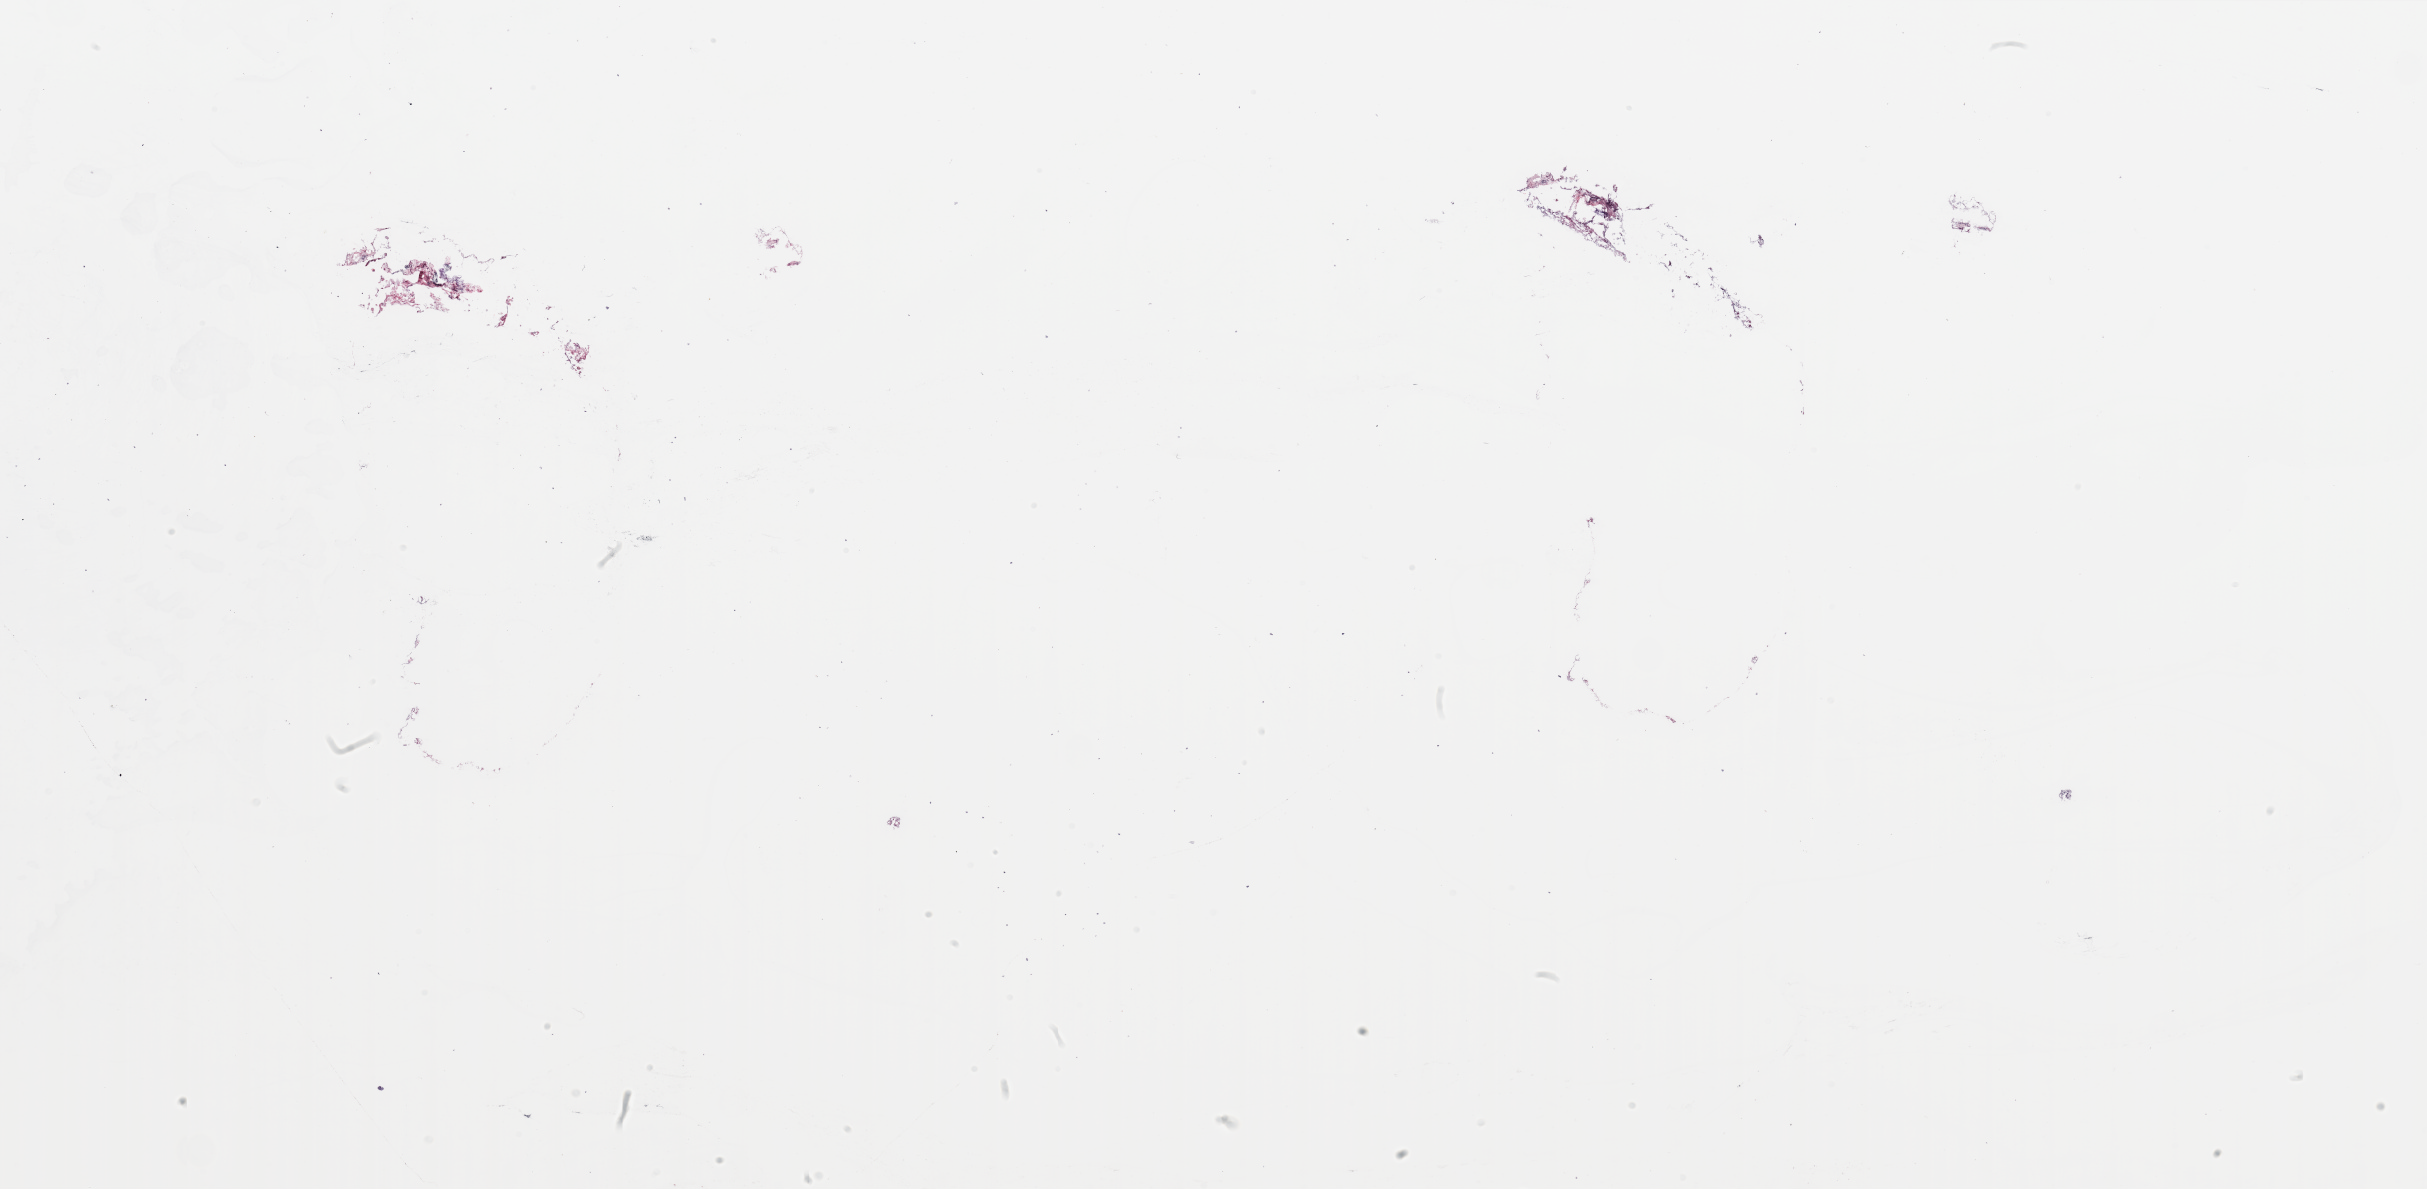
Whole-slide histology image, H&E-stained, whole scanned area (about 38.4 x 18.8 mm, acquisition: 20x scan) shown as a low-resolution overview, breast, tissue type not recorded.
Patient diagnosis (cohort enrolment): breast cancer (breast).